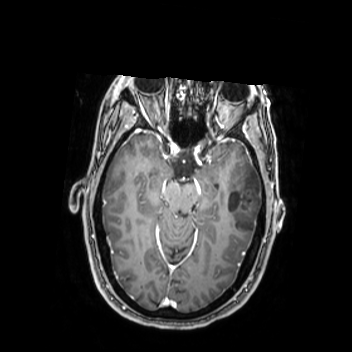
Brain MRI from a brain-tumour surgery series, one axial slice; T1-weighted post-contrast; 352 × 352 image matrix, field of view 280 × 280 mm. From the clinical record (not read from this slice): histopathology: Oligodendroglioma; WHO grade: 2; IDH mutation: yes.
Structures marked on this image (manually delineated by an expert):
- tumour: bounding box <224,163,262,236> (left, top, right, bottom; pixels)